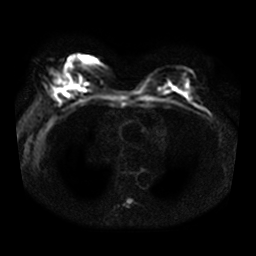
Breast MRI, one axial slice. Slice 19 of 36 in the series (ordered by position). Diffusion-weighted series; image 2 of 4 stored at this slice position (different b-values; order by instance number). 3 T. 5 mm slice thickness. 256 × 256 image matrix. Female patient.
Outlined on this slice (manually delineated by an expert):
- tumour on diffusion-weighted imaging: bounding box (x1, y1, x2, y2) in pixels: (62, 82, 77, 98)